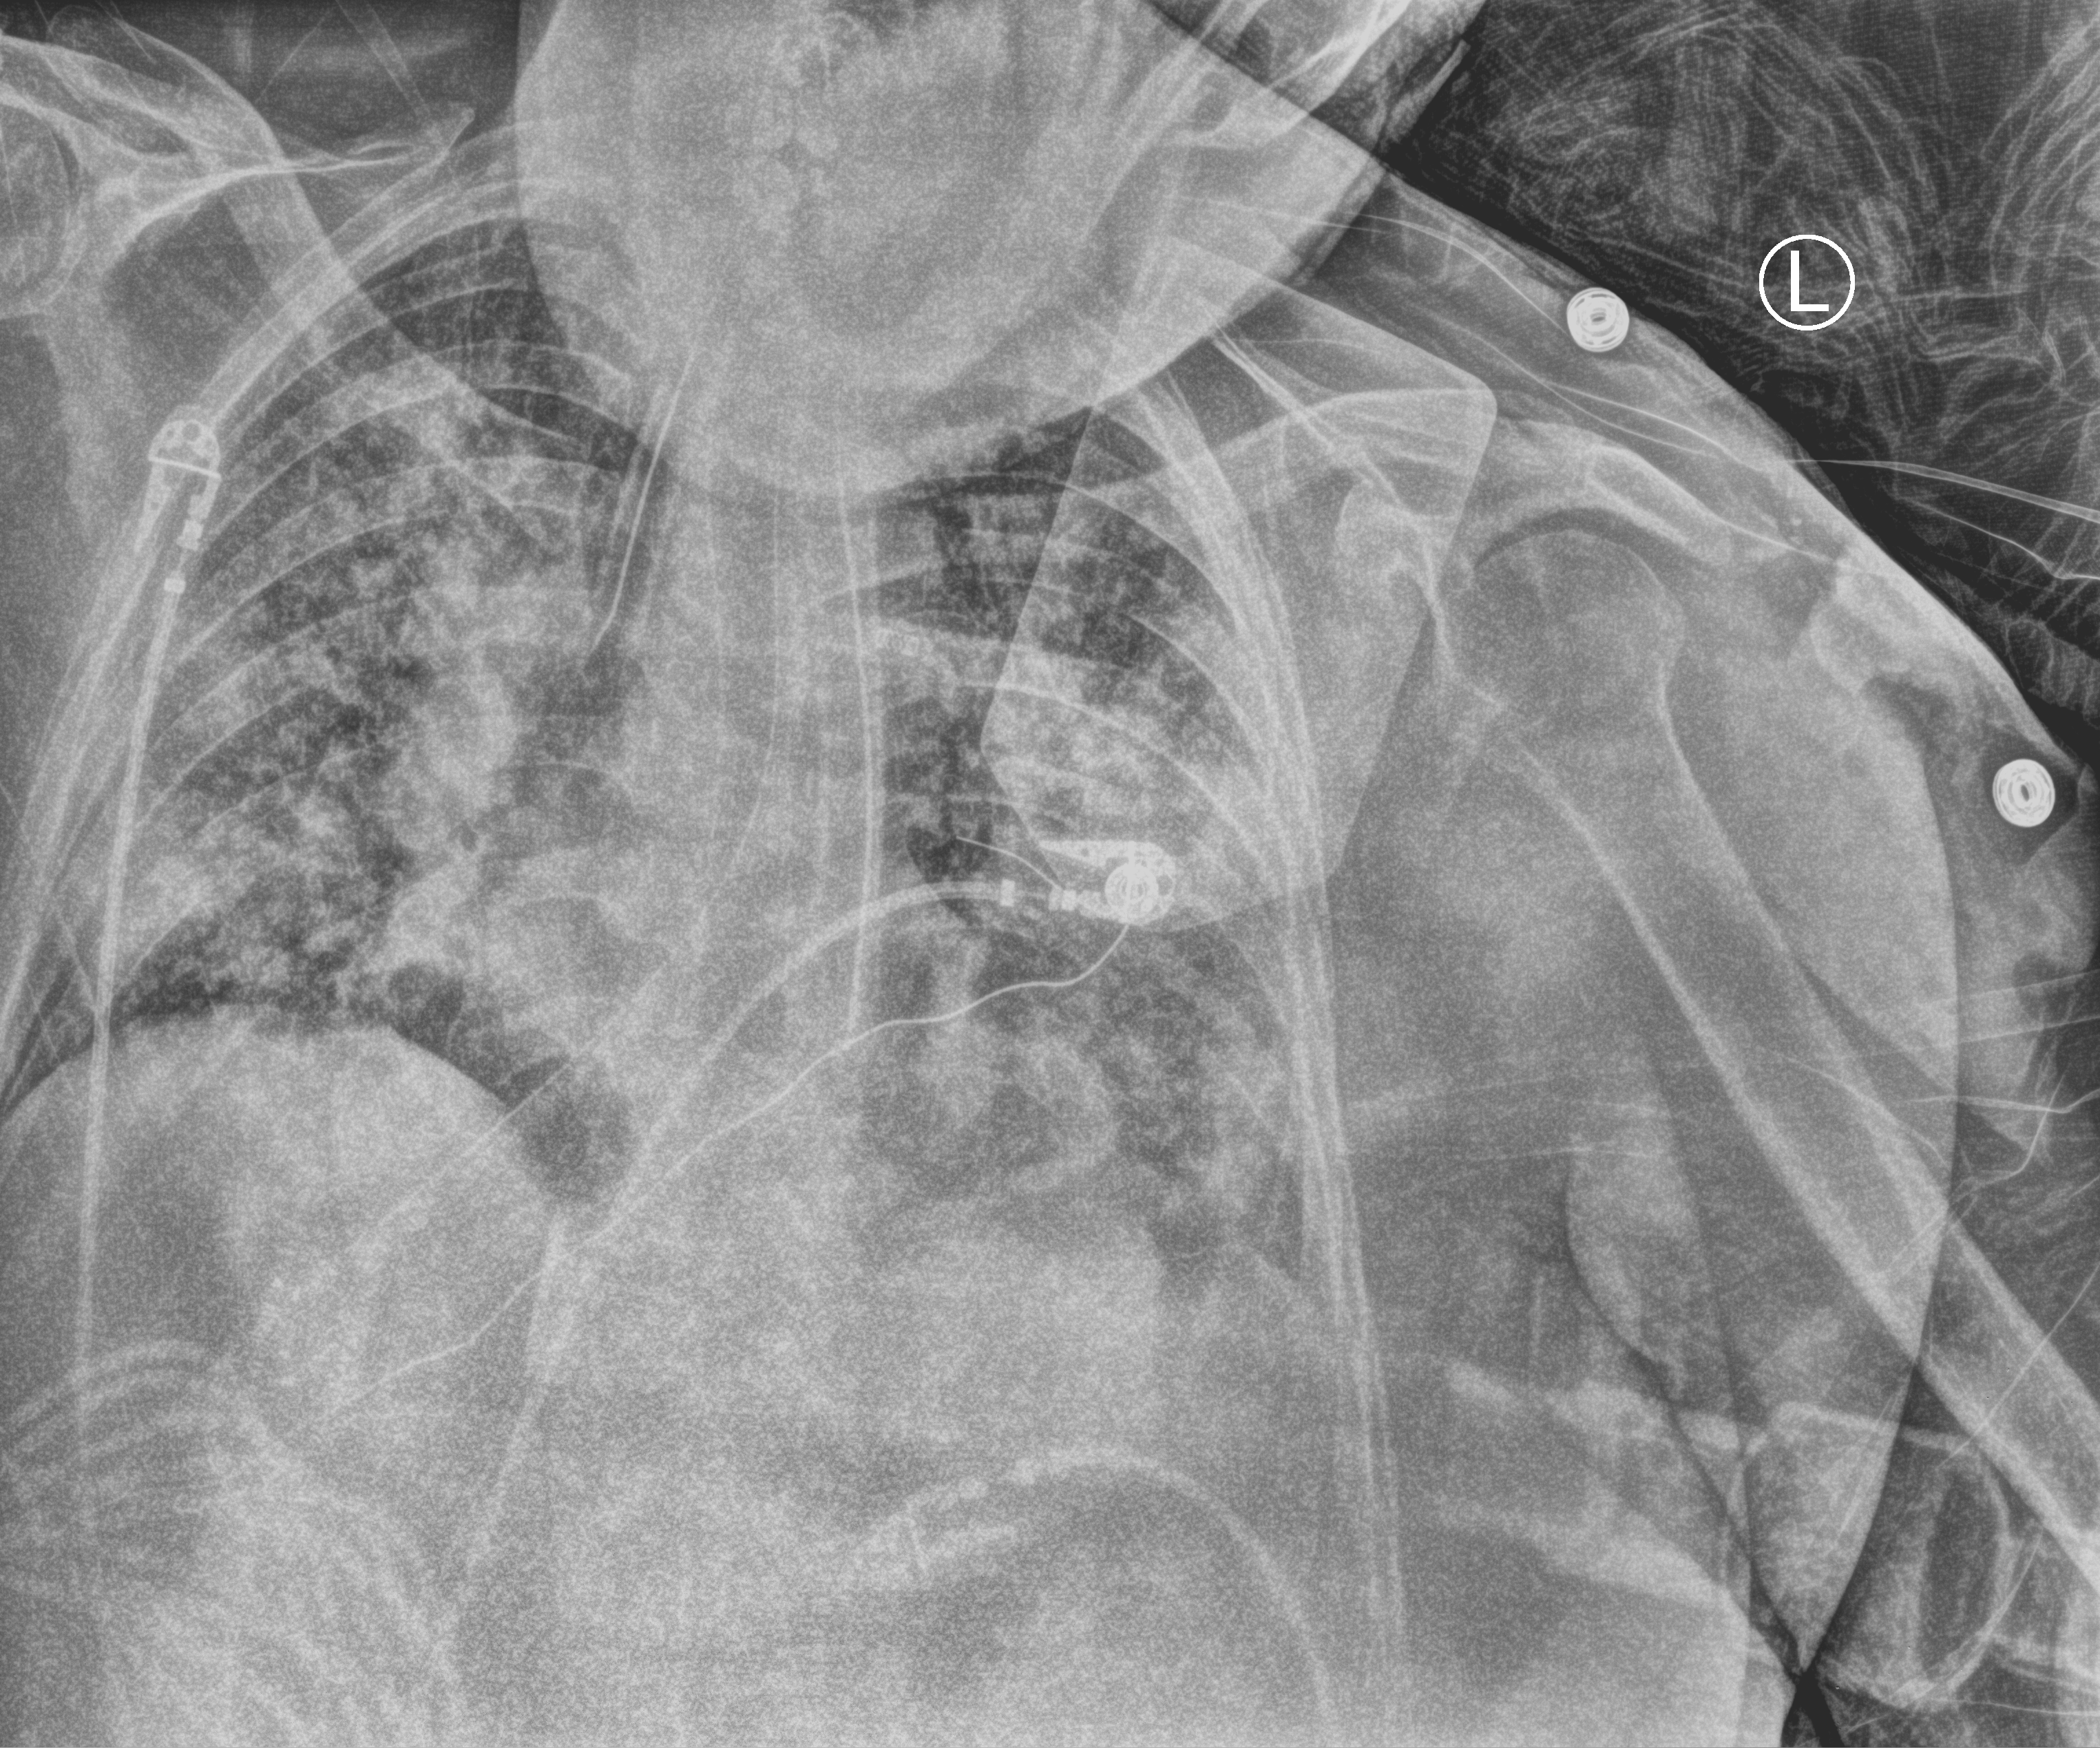
Portable chest radiograph; anteroposterior (AP) projection. Patient hospitalised with COVID-19; female, aged 60–74 years.
Admission-level facts for this patient (not findings on this image; timing relative to this image not recorded): length of hospital stay: 19 days; diabetes (admission record): no; chronic kidney disease (admission record): no.